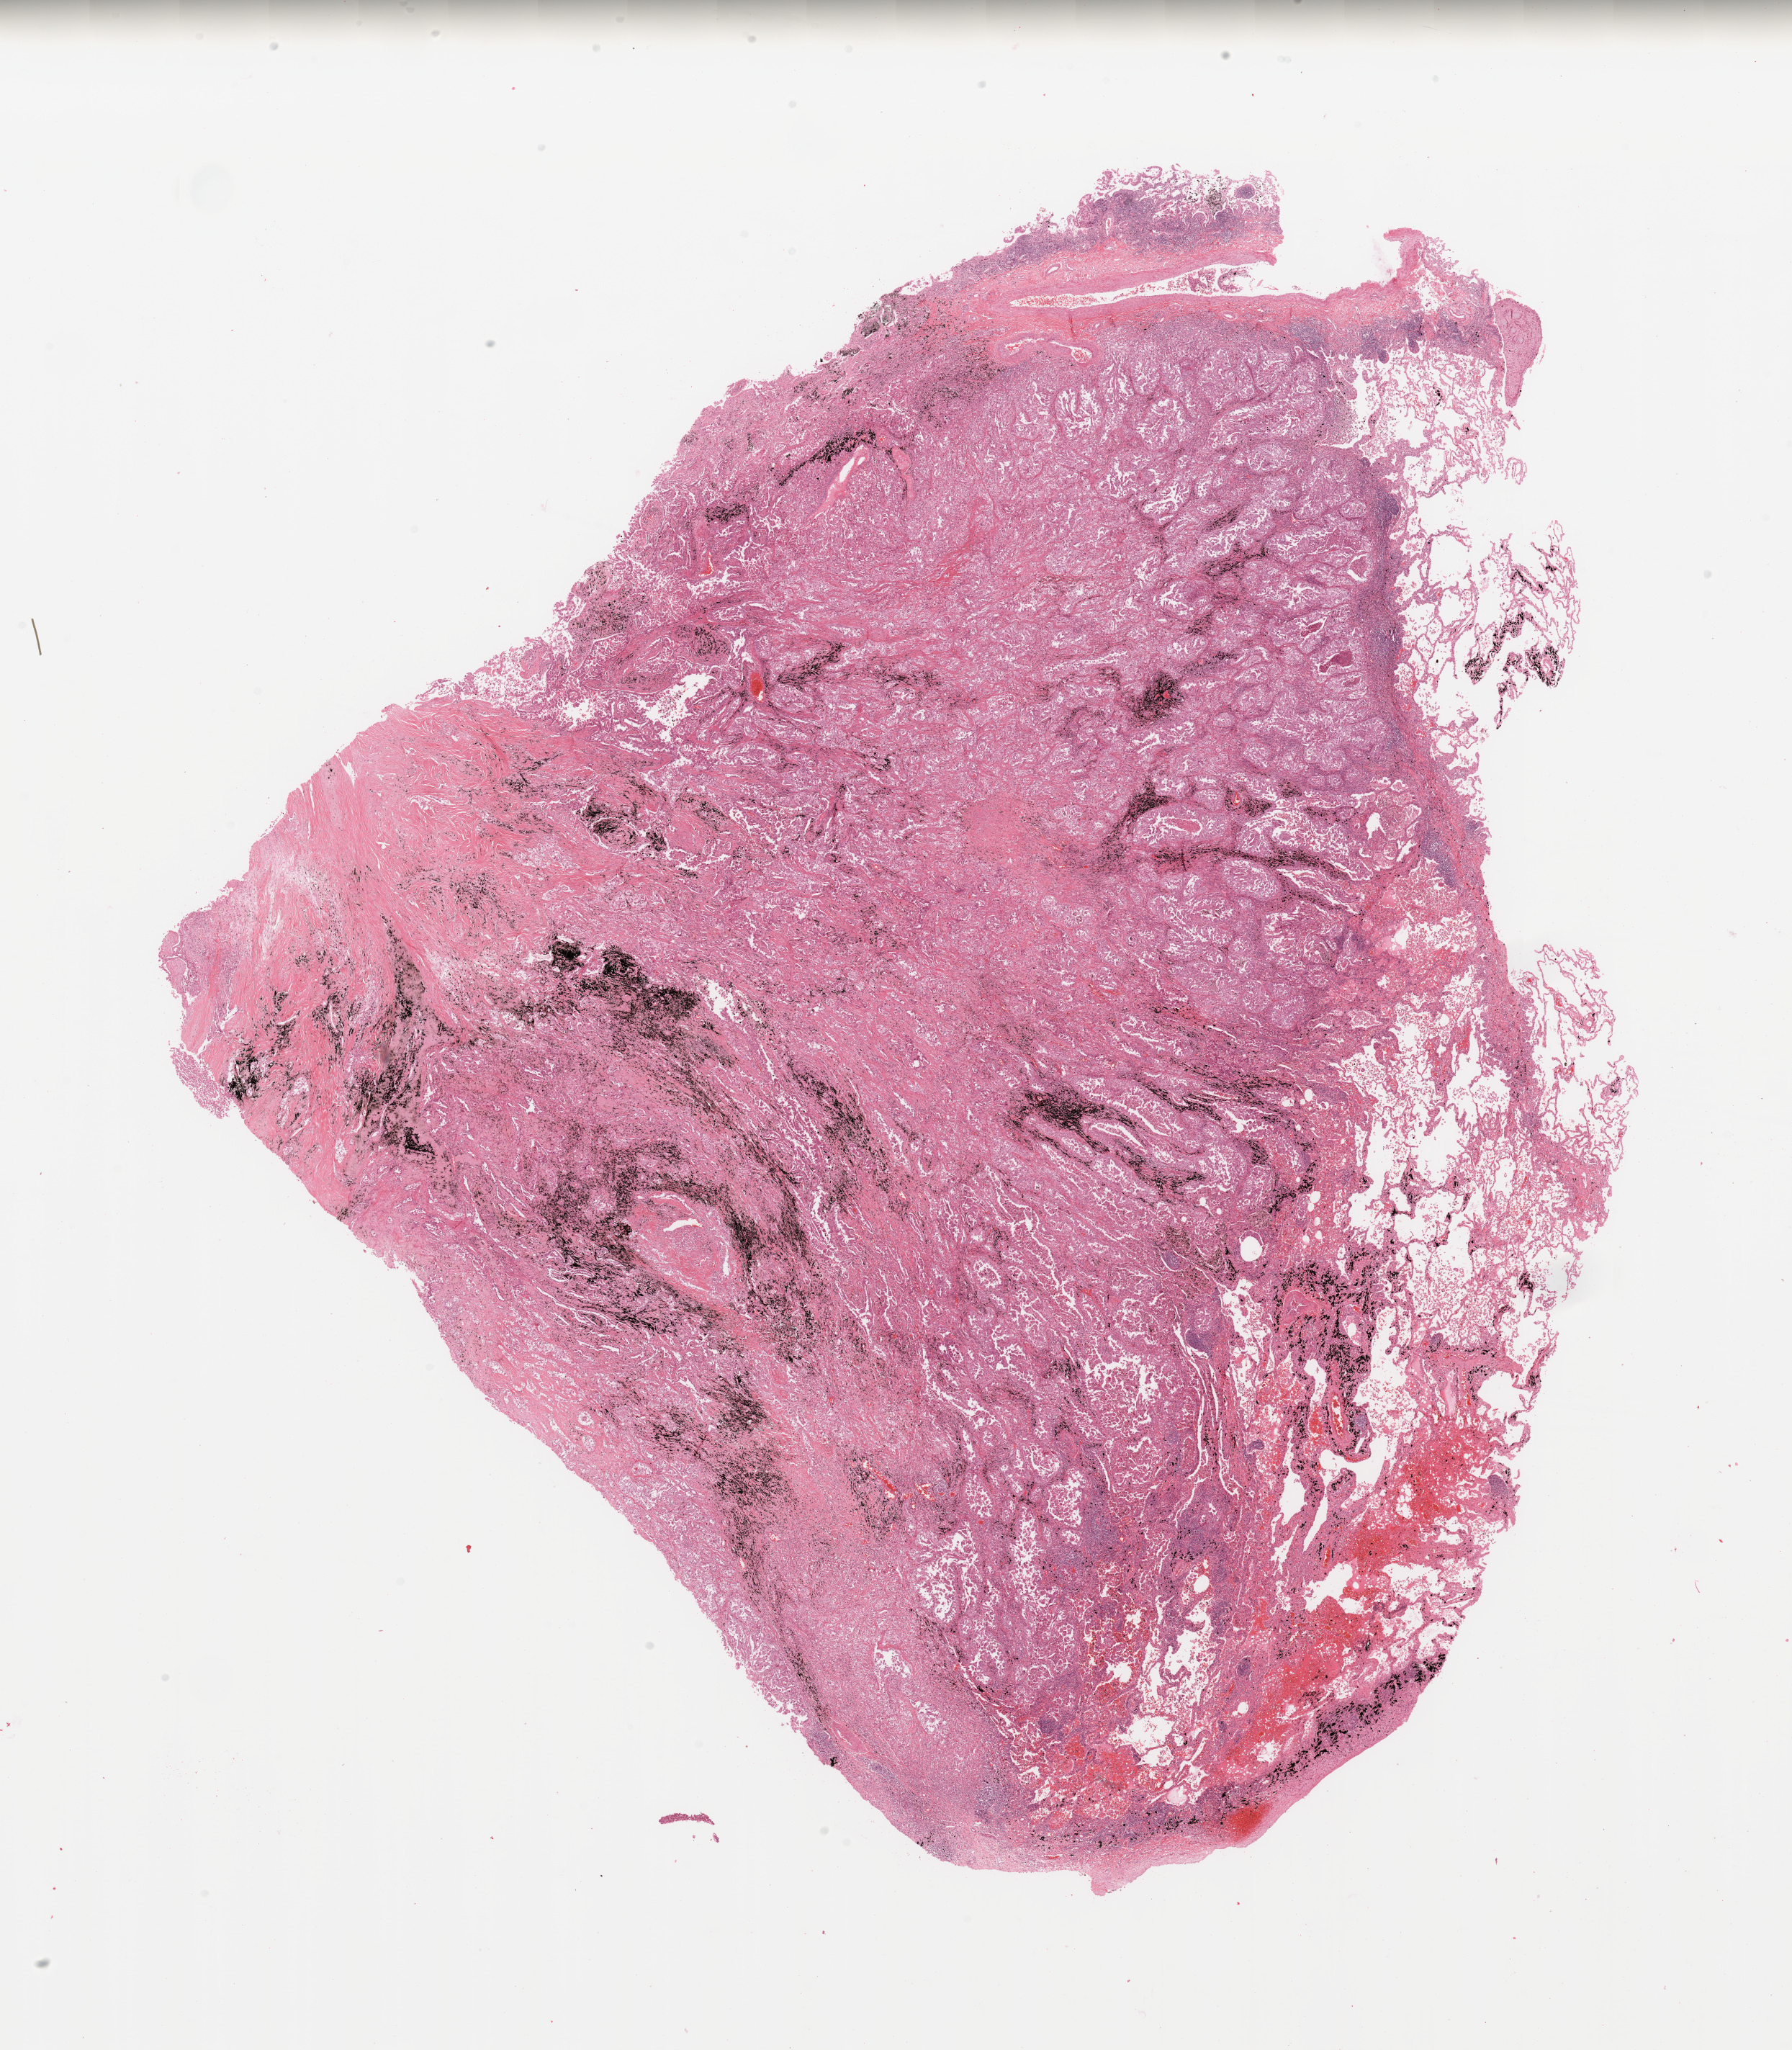
H&E whole-slide image, shown as a low-resolution overview of the whole scanned area (about 19.7 x 22.5 mm). Tumour tissue sample, sampled site: lung. 65-year-old male patient. Histologic grade: G3 (poorly differentiated). Pathologist review of this section (percent, as recorded): tumour nuclei 70%, necrosis 10%.
Histologic diagnosis: Adenocarcinoma, NOS. AJCC pathologic stage: IB.